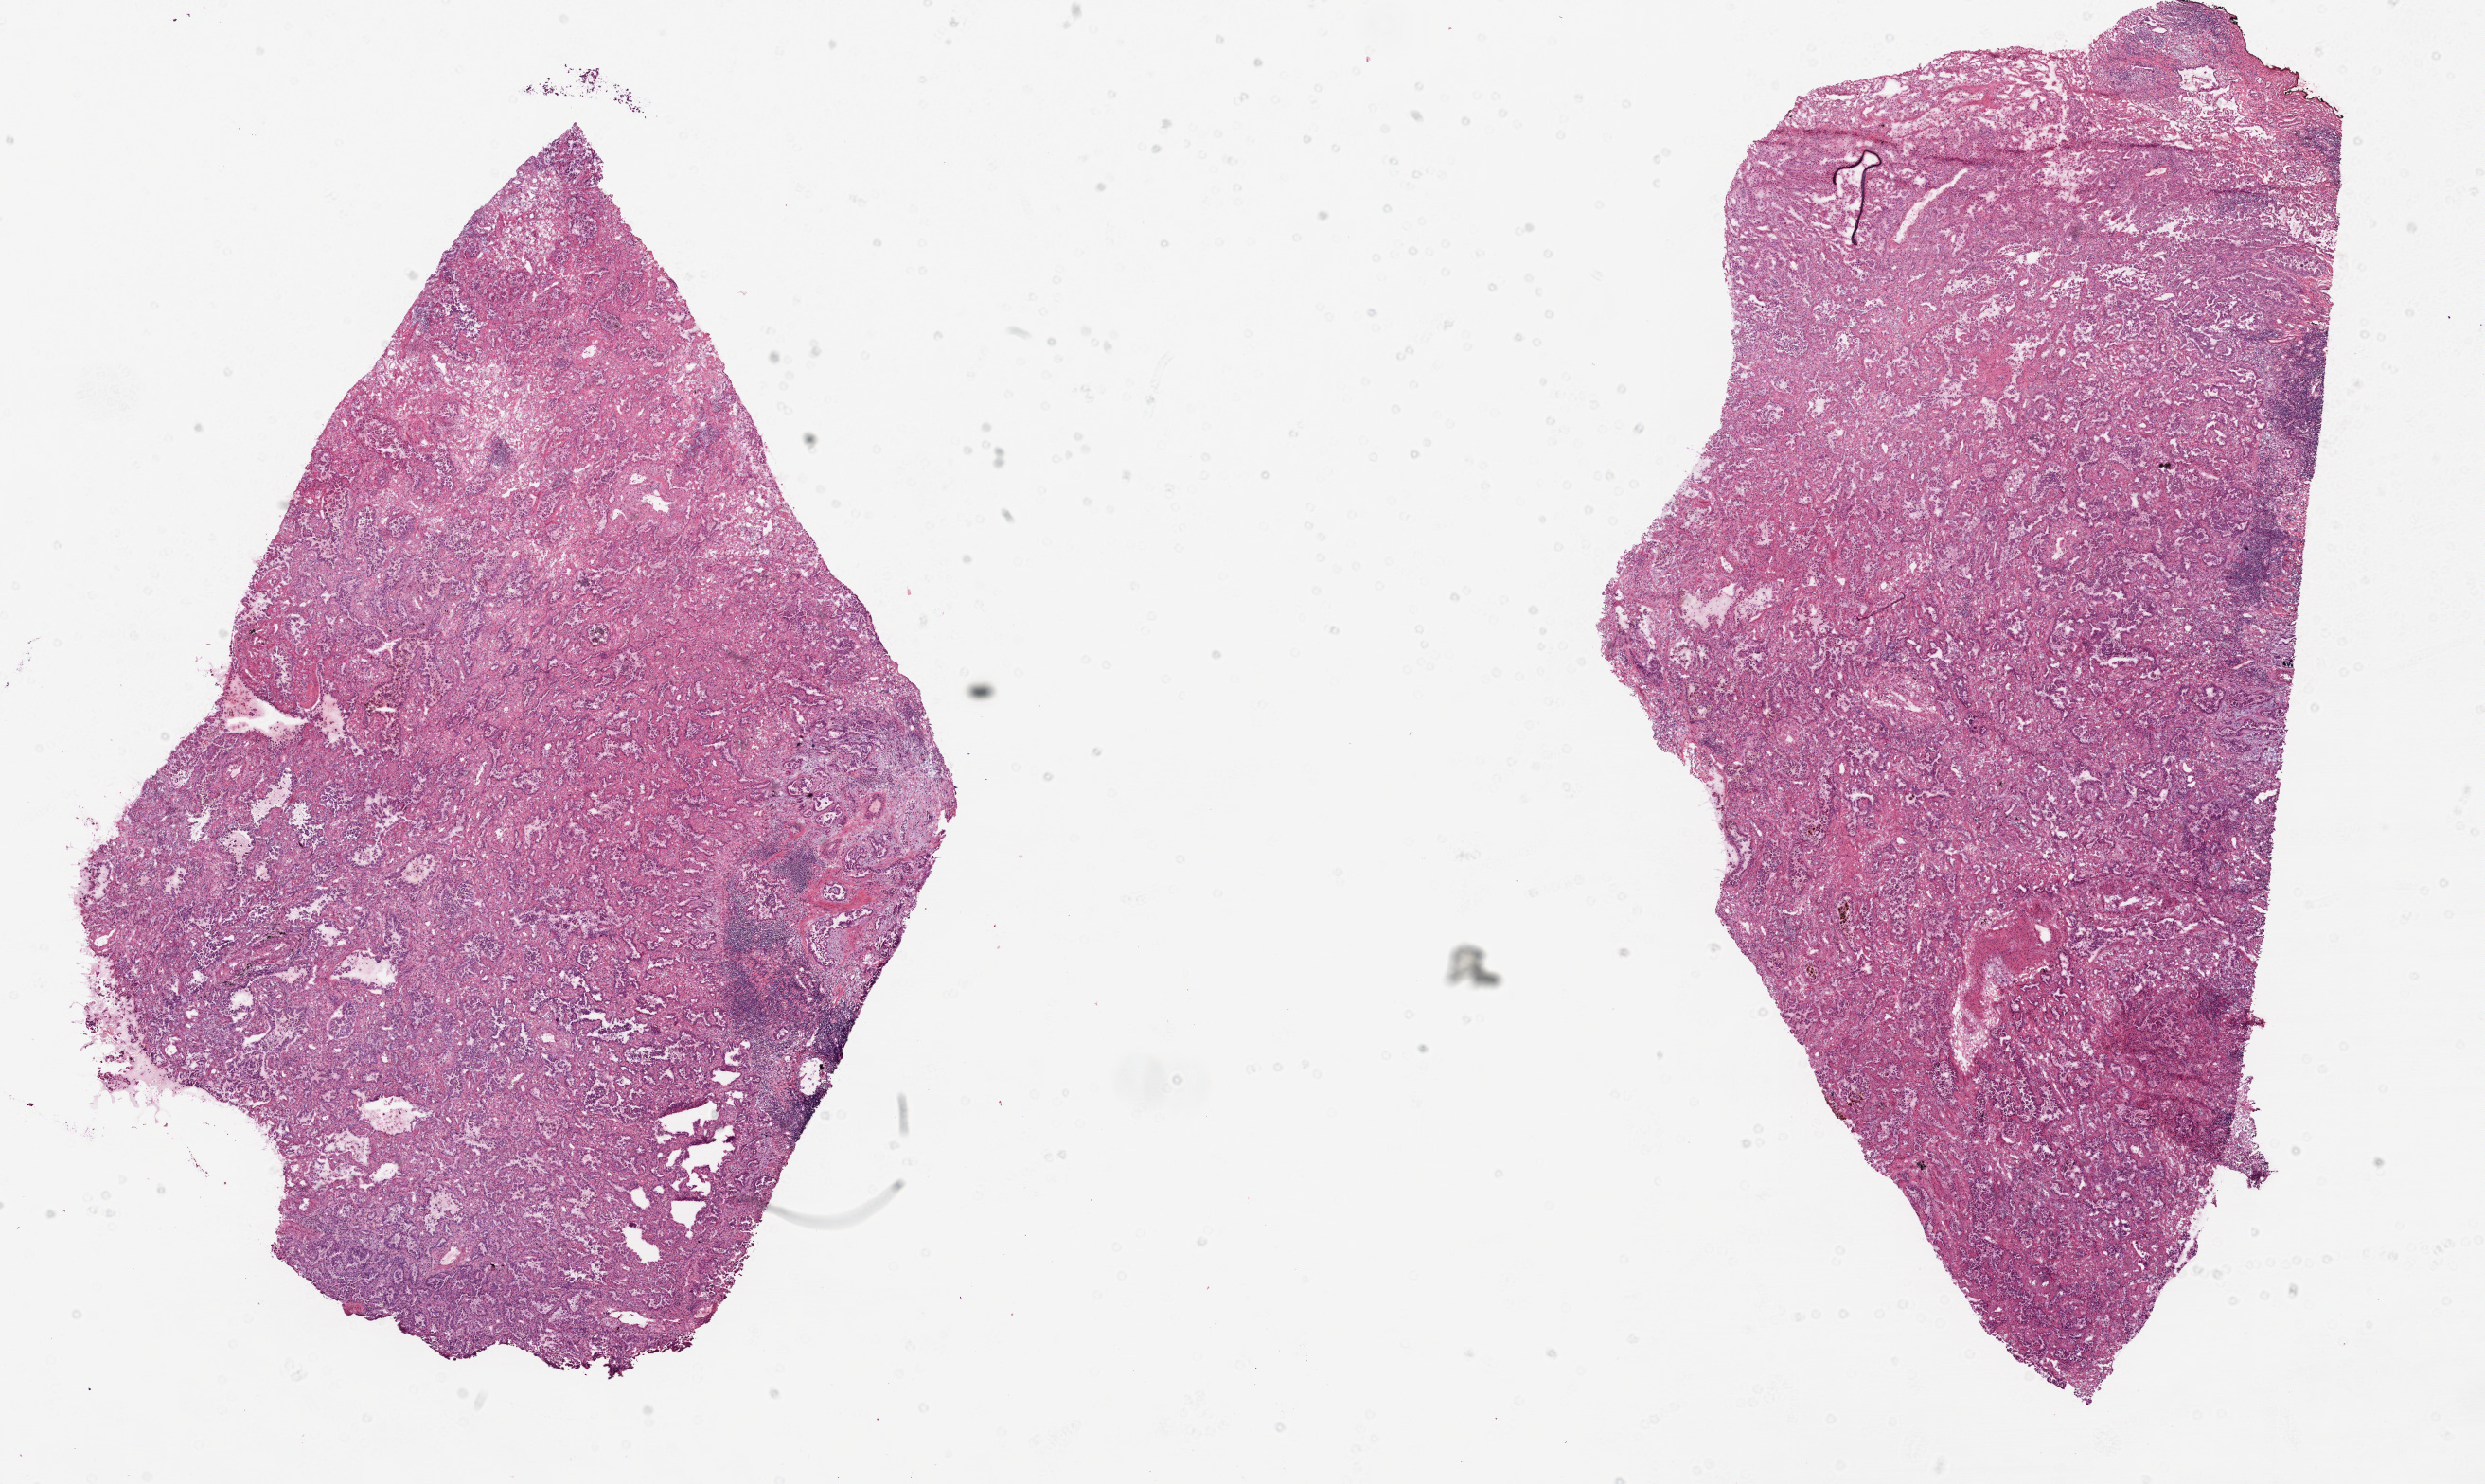
Whole-slide histology image, H&E-stained — shown as a low-resolution overview of the whole scanned area (about 21.1 x 12.6 mm, slide scanned at 20x); frozen section; primary tumour sample from the lung. Female, age 67 years at initial diagnosis. Slide review estimates, as recorded: tumour cells 70%, tumour nuclei 70%.
Histologic diagnosis: Adenocarcinoma, NOS (upper lobe, lung).